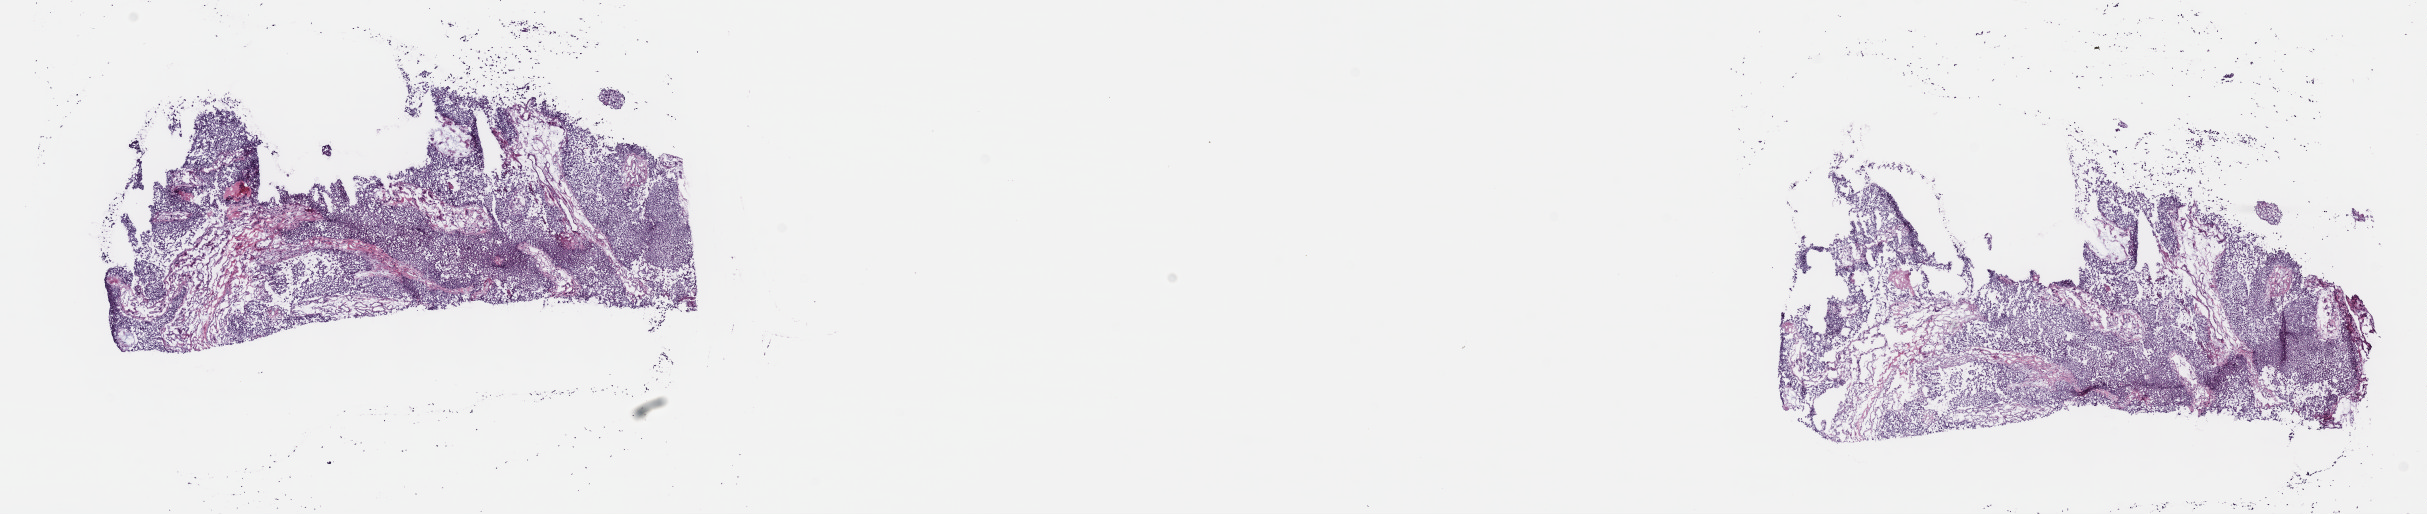
Digitized H&E-stained tissue section (whole slide) — whole scanned area (about 19.6 x 4.2 mm) shown as a low-resolution overview, frozen section from the top of the tissue portion, primary tumour sample from the bladder. Male, age 69 years at initial diagnosis. Histologic grade: high grade. Composition of this section per pathologist review: tumour cells 100%, tumour nuclei 75%, normal cells 0%, stromal cells 0%, necrosis 0%. Inflammatory infiltration, as recorded: lymphocyte infiltration 3%, monocyte infiltration 0%, neutrophil infiltration 0%.
TNM: T3a N0 M0. Histologic diagnosis: Transitional cell carcinoma. AJCC pathologic stage: III. Lymph nodes positive (case pathology): 0 of 18 examined.